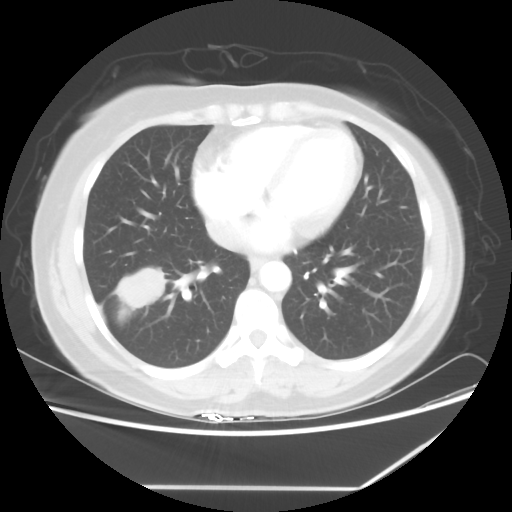
Chest CT, one axial slice. Position 24 of 60 along the scan axis. Reconstruction kernel STANDARD. 100 kVp. Lung window (W 1500 / L -600 HU). 5 mm slice thickness. 512 × 512 image matrix, field of view 374 × 374 mm. Female patient, age 42 years. From the clinical record (not read from this slice): clinical TNM (as recorded): T2 N1 M0.
Structures marked on this image (rectangle marked by the reading radiologist):
- lung tumour (recorded histology: adenocarcinoma): bounding box (x1, y1, x2, y2) in pixels: (104, 264, 169, 312)